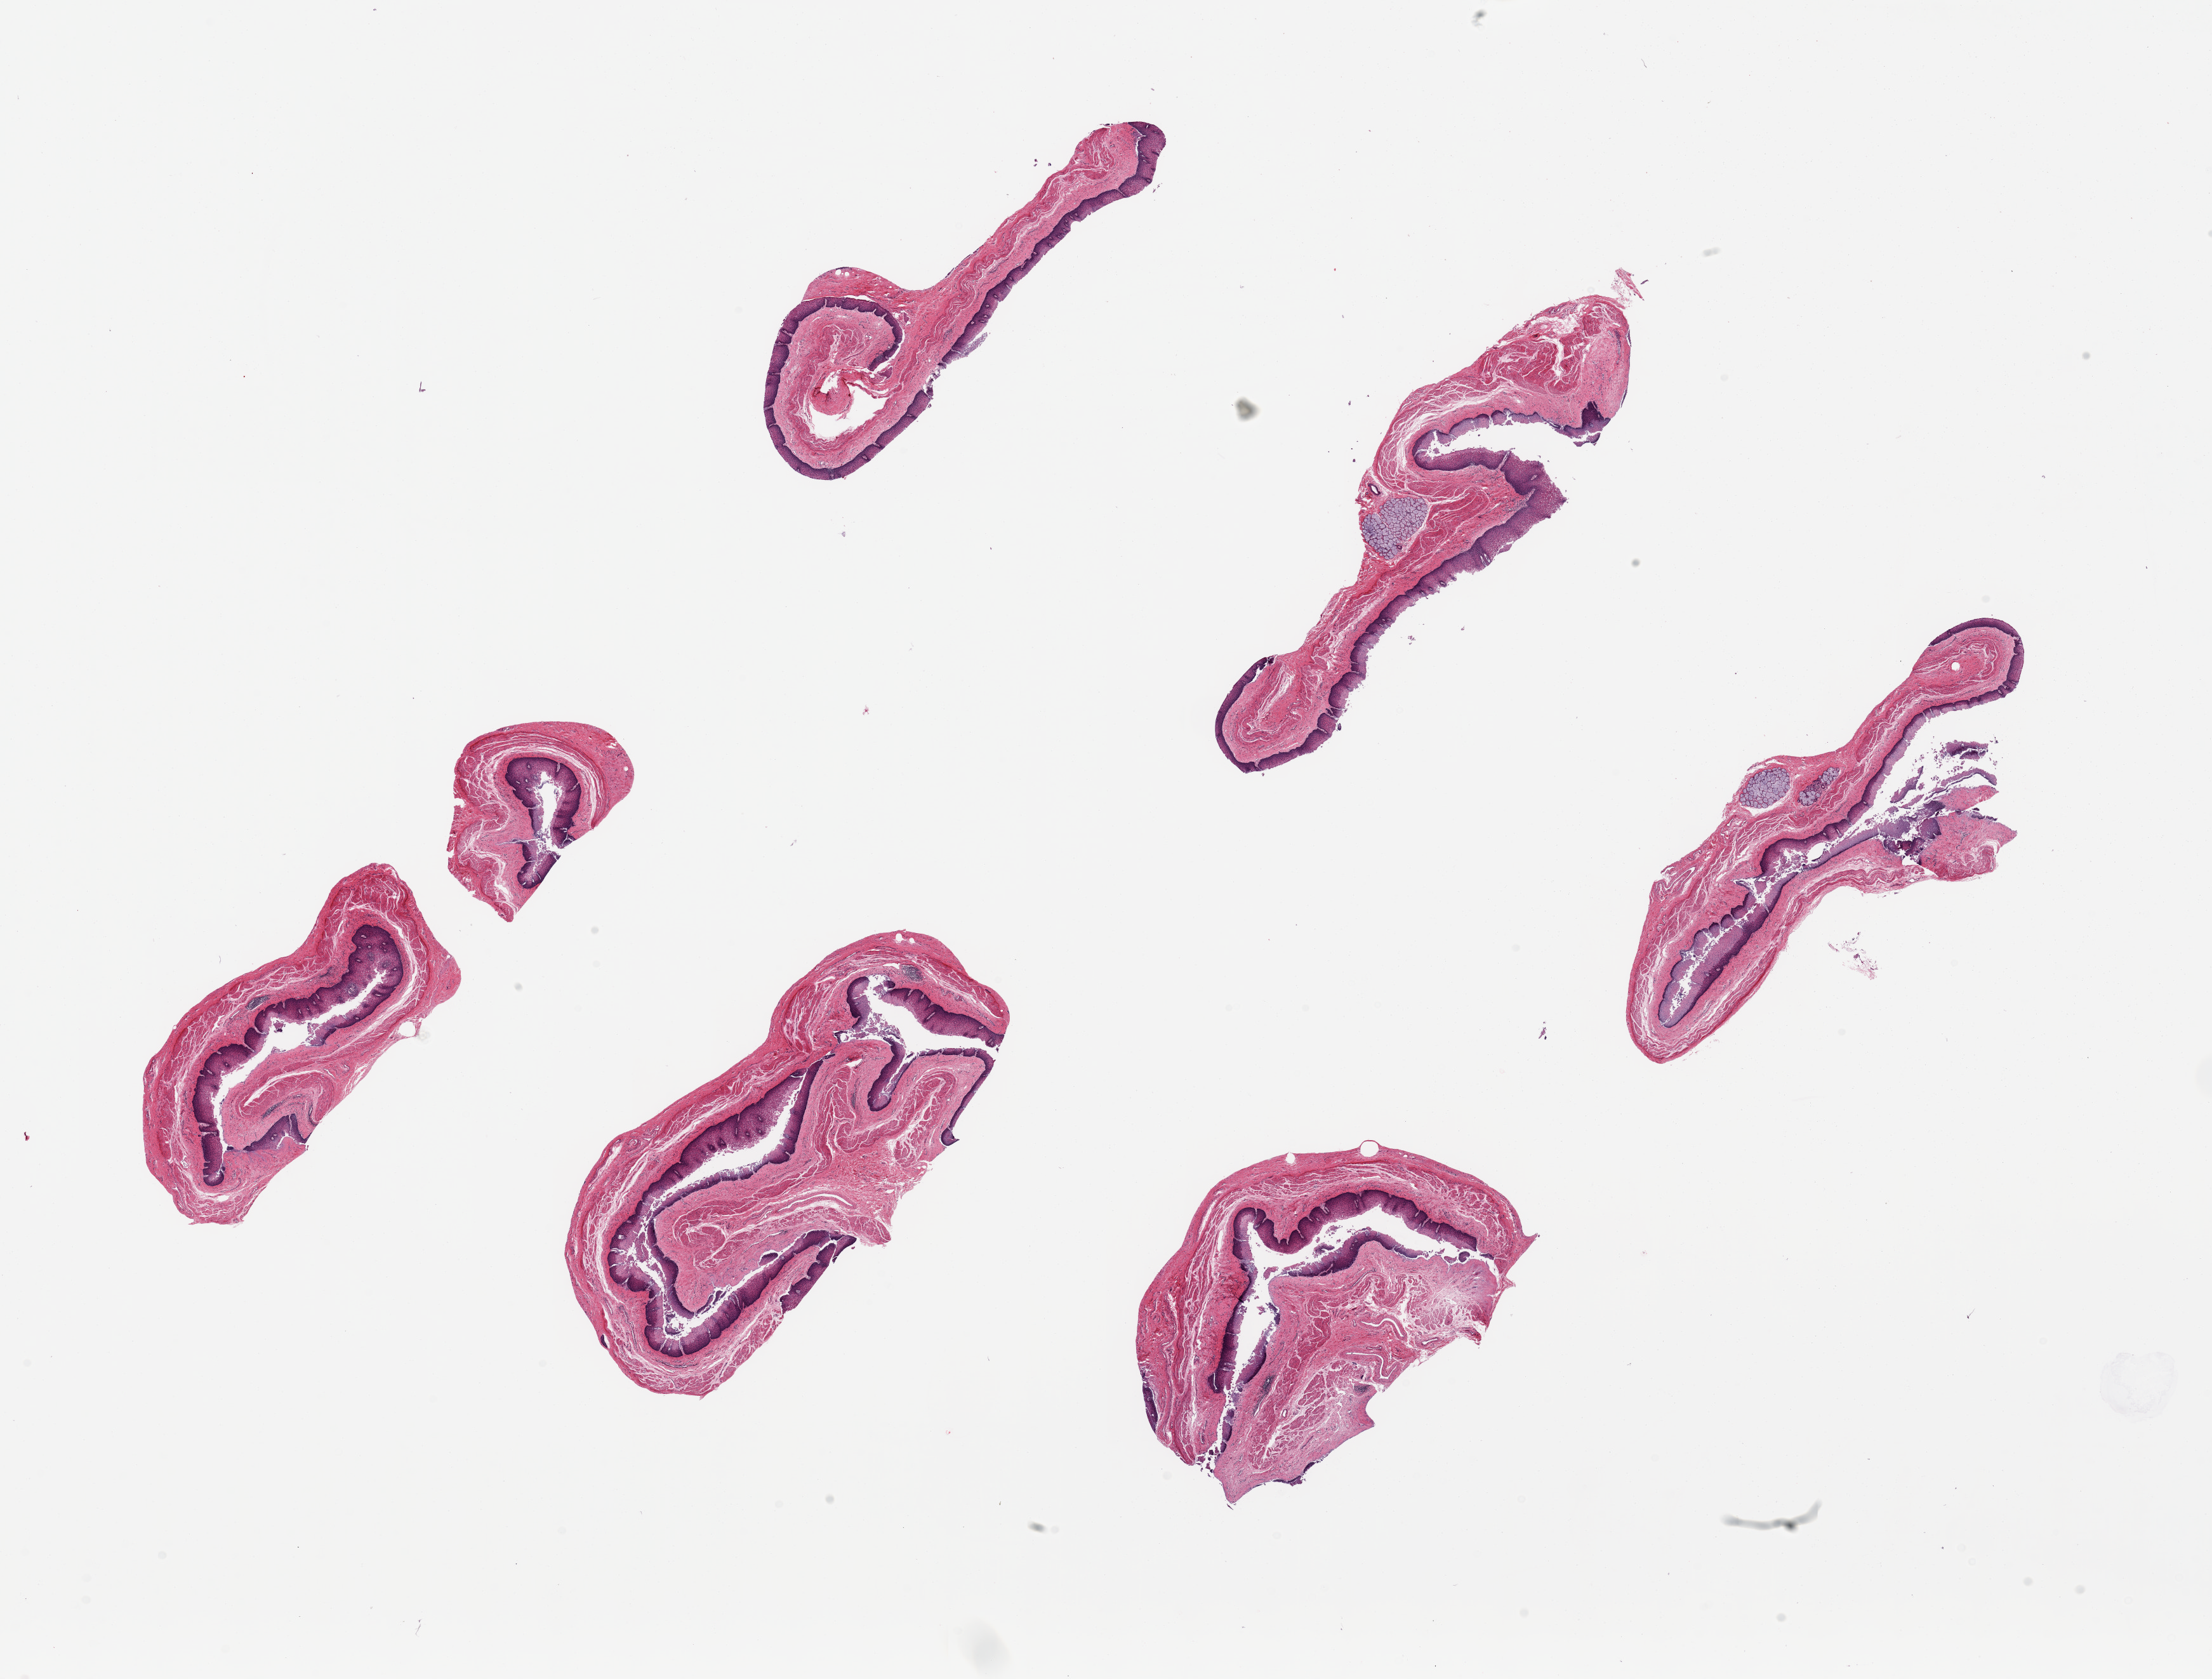
Whole-slide image, haematoxylin and eosin stain, brightfield, a low-resolution overview of the entire scanned area, about 27.6 x 20.9 mm, PAXgene-fixed, paraffin-embedded tissue, target tissue: esophageal mucous membrane, donor tissue sample. Donor: female.
- review note (as recorded): 6 pieces ~7.5x1-2 mm